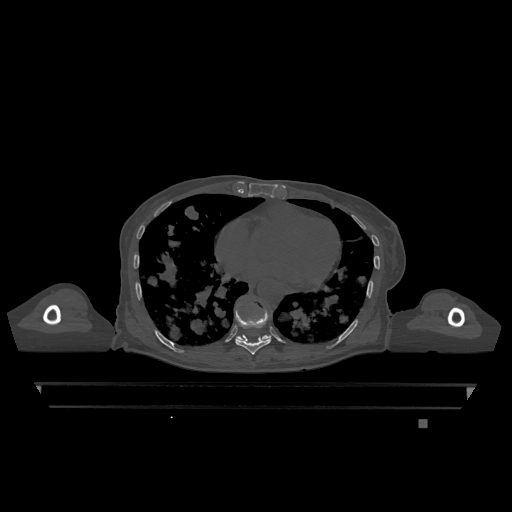
CT including the spine, one axial slice; slice 679 of 1317 in the series (ordered by position); bone window (W 1800 / L 400 HU); 0.5 mm slice thickness; 512 × 512 image matrix. Patient: female, 74 years. From the clinical record (not read from this slice): primary cancer: lung.
Structures marked on this image (semi-automatic segmentation, software-assisted and operator-edited):
- T10 vertebra: bounding box (x1, y1, x2, y2) in pixels: (236, 335, 271, 340)
- T9 vertebra: (235, 302, 271, 355)